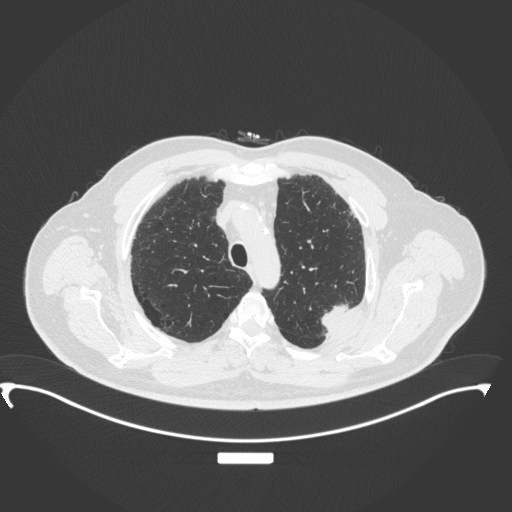
Chest CT, one axial slice. Position 282 of 350 along the scan axis. 120 kVp. Lung window (W 1500 / L -600 HU). 1 mm slice thickness. 512 × 512 image matrix, field of view 459 × 459 mm. Male patient, age 64 years. Case-level facts recorded for this patient, not image findings: clinical TNM (as recorded): T1c N1 M1.
Annotated regions visible in this slice (rectangle marked by the reading radiologist):
- lung tumour (recorded histology: adenocarcinoma): bounding box [x1, y1, x2, y2] px = [320, 297, 349, 334]